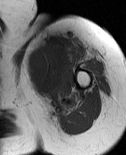
MRI of an extremity soft-tissue mass, one axial slice. Position 58 of 86 along the scan axis. MR volume resampled by the dataset authors to the PET/CT grid (not the native acquisition matrix). 3.27 mm slice thickness. 126 × 155 image matrix, field of view 123 × 151 mm. Female patient. Case-level facts recorded for this patient, not image findings: histological type: pleiomorphic leiomyosarcoma; grade: high; site of the primary tumour: left biceps.
Annotated regions visible in this slice (expert contour drawn on MRI and transferred to this co-registered scan by the dataset authors):
- gross tumour volume including surrounding oedema: bounding box <27,40,73,110> (left, top, right, bottom; pixels)
- gross tumour volume (mass): <27,40,71,96>